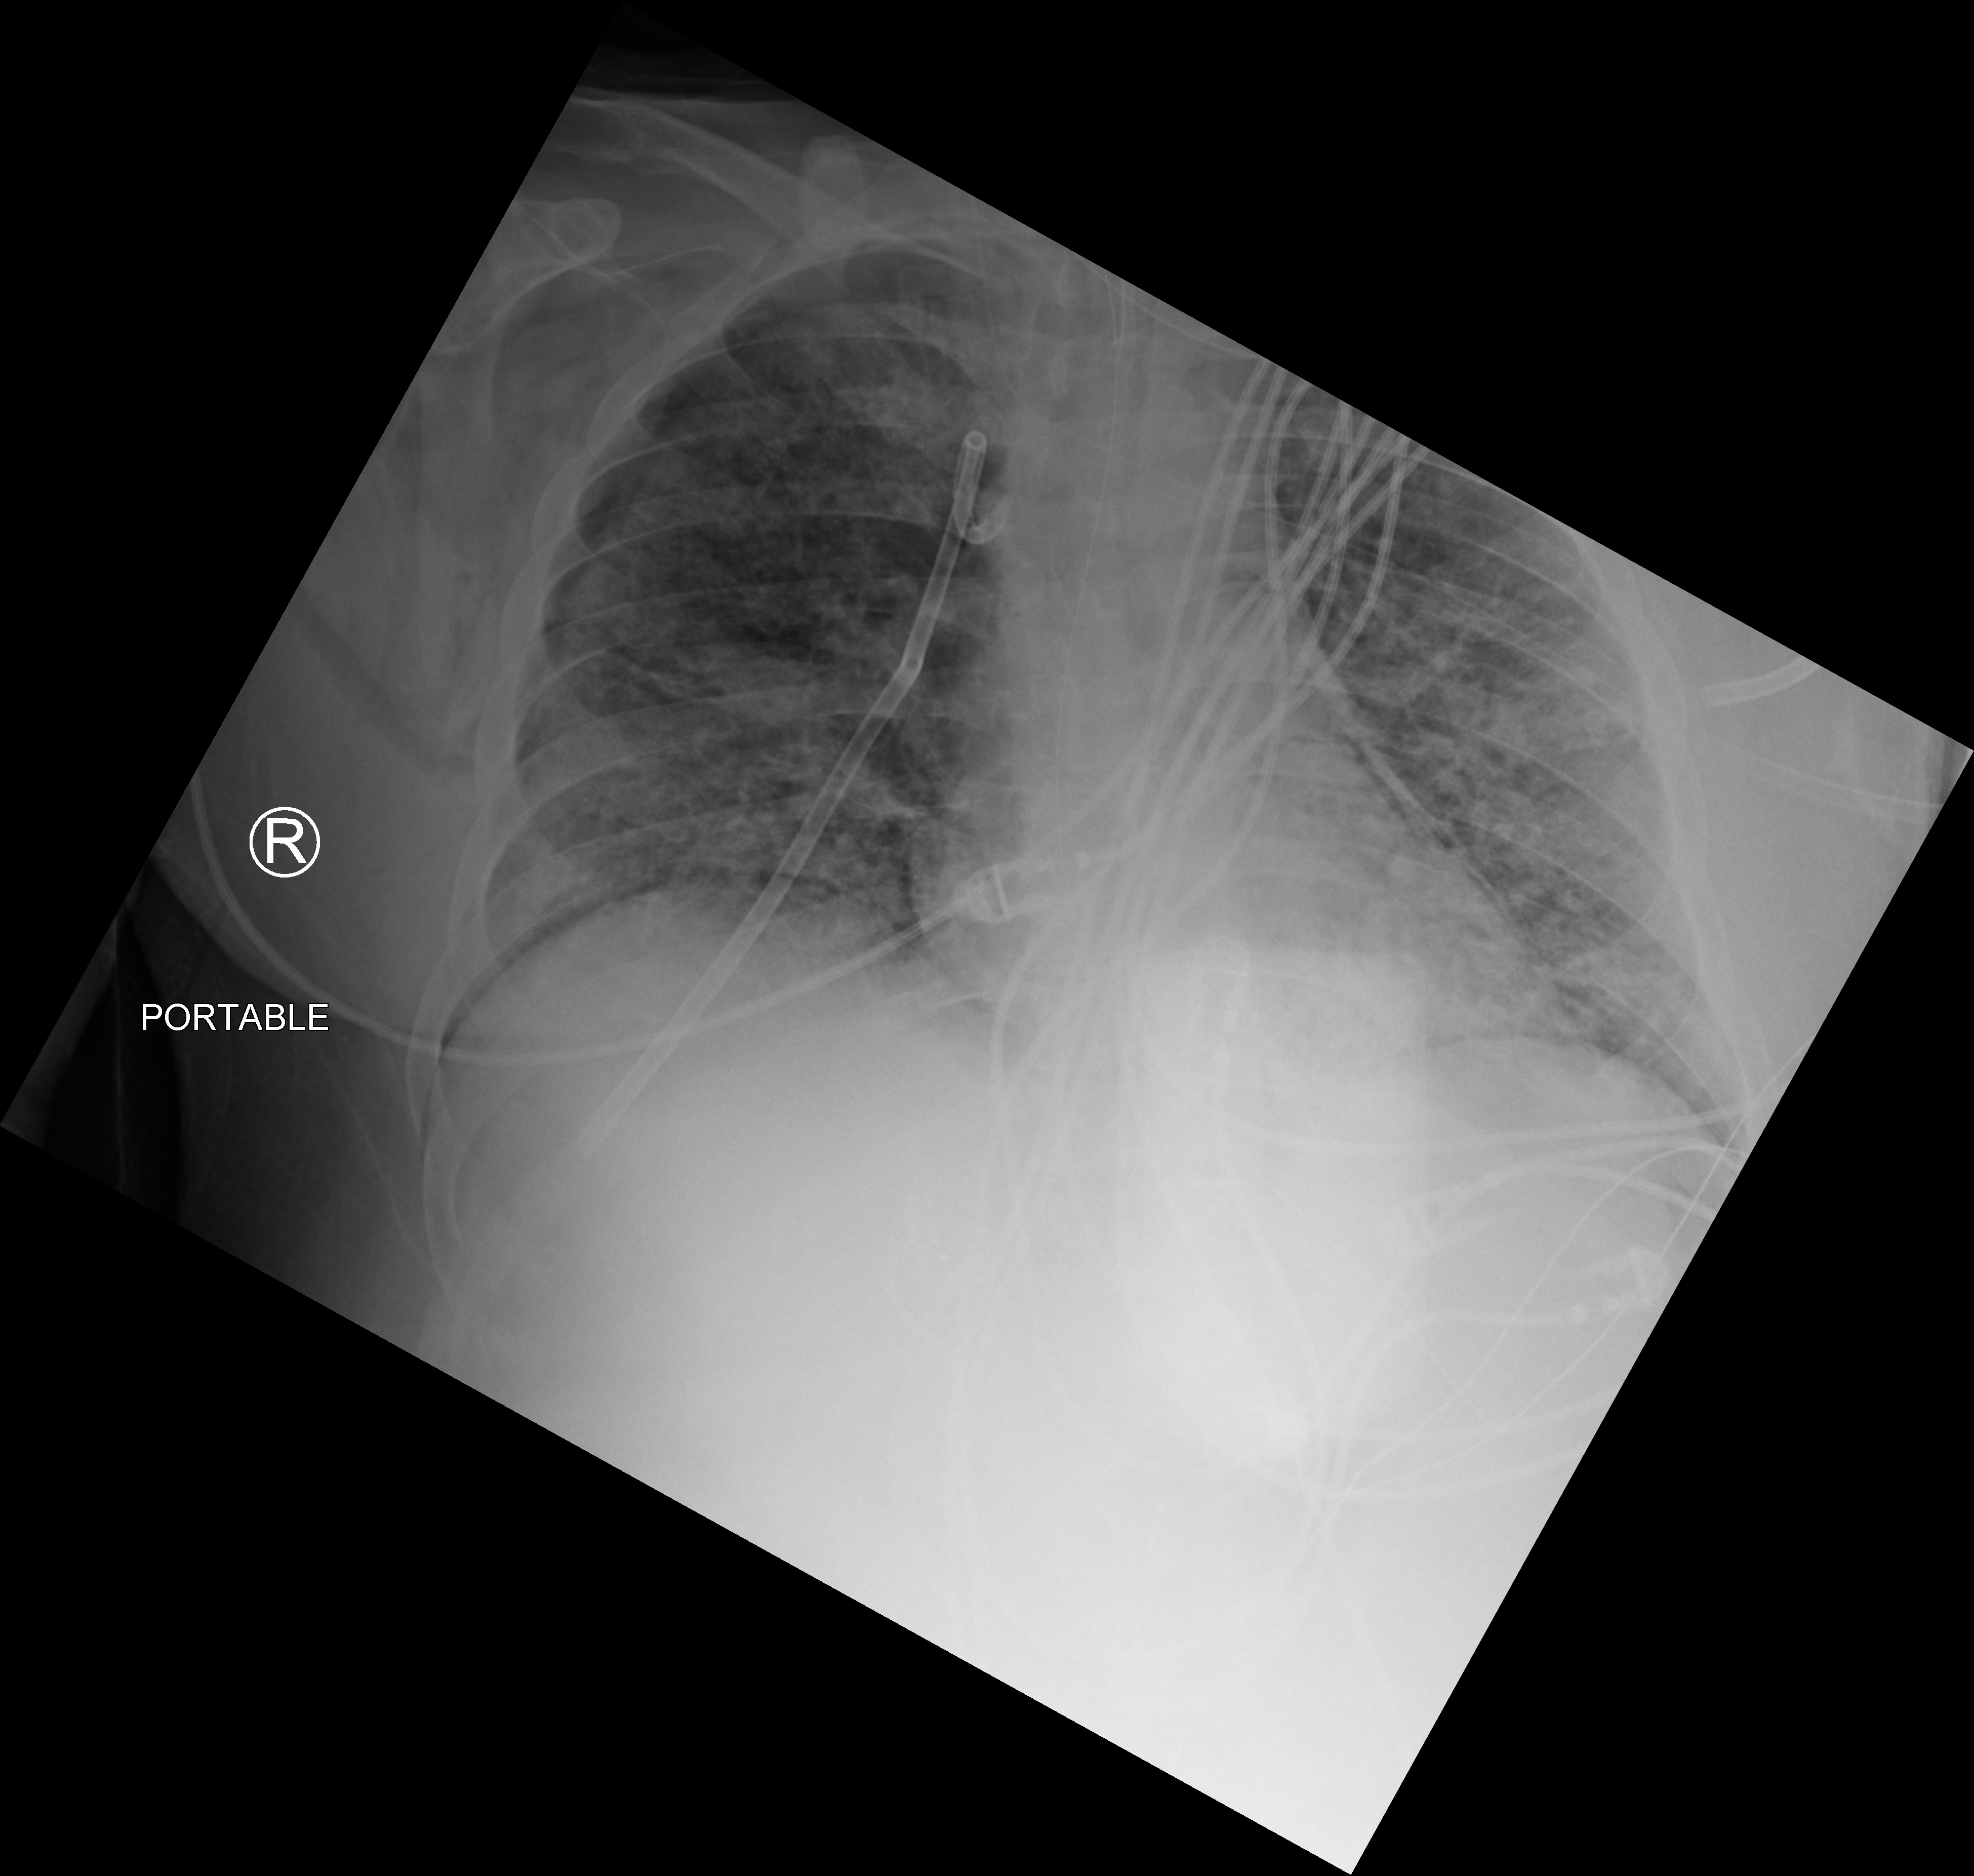
Chest X-ray (portable); anteroposterior (AP) projection. Adult patient hospitalised with COVID-19, age 18–59 years.
From the hospital-stay record, not from the radiograph (when in the stay this image was taken is not recorded):
- mechanically ventilated during this hospital stay: yes
- length of hospital stay: 31 days
- admitted to intensive care during this hospital stay: yes